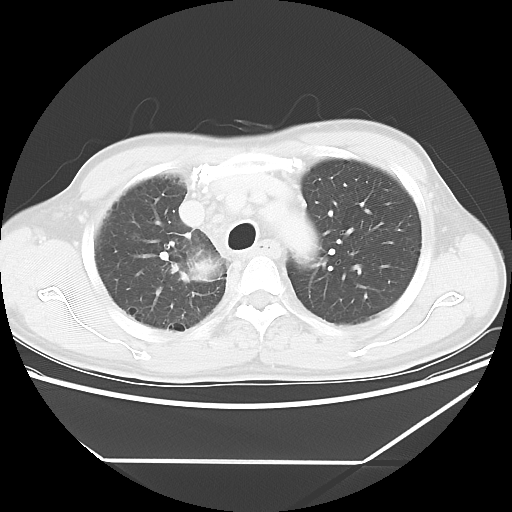
Chest CT, one axial slice; position 46 of 60 along the scan axis; lung window (W 1500 / L -600 HU); 512 × 512 image matrix, field of view 367 × 367 mm. Patient: male, 58 years. From the clinical record (not read from this slice): clinical TNM (as recorded): T2 N2 M0.
Outlined on this slice (rectangle marked by the reading radiologist):
- lung tumour (recorded histology: squamous cell carcinoma): bounding box (x1, y1, x2, y2) in pixels: (169, 239, 227, 299)